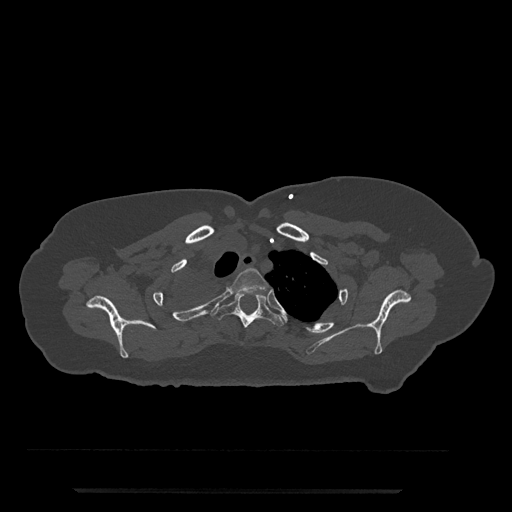
CT including the spine, one axial slice; reconstruction kernel Br40s/3; 120 kVp; bone window (W 1800 / L 400 HU); 0.5 mm slice thickness; 512 × 512 image matrix, field of view 440 × 440 mm. Patient: female, 51 years. From the clinical record (not read from this slice): primary cancer: neuro; vertebrae with lytic lesions (as recorded): T8.
Annotated regions visible in this slice (semi-automatically segmented with operator editing):
- T2 vertebra: bounding box <228,268,268,294> (left, top, right, bottom; pixels)
- T3 vertebra: <211,292,285,328>